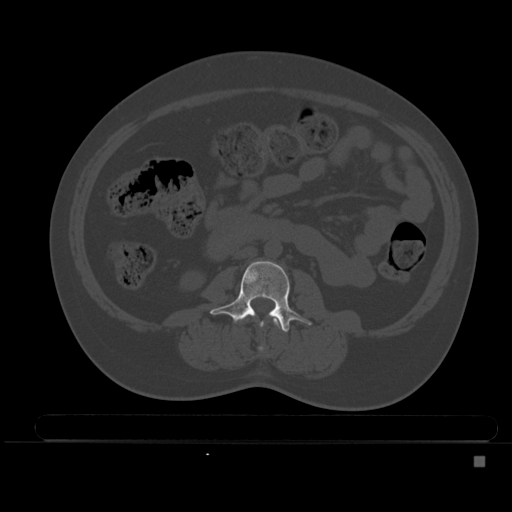
CT including the spine, one axial slice; position 155 of 495 along the scan axis; bone window (W 1800 / L 400 HU); 512 × 512 image matrix, field of view 404 × 404 mm. Female patient, age 33 years. From the clinical record (not read from this slice): primary cancer: breast; vertebrae with lytic lesions (as recorded): T1.
Annotated regions visible in this slice (semi-automatically segmented with operator editing):
- L2 vertebra: box from (x=244, y=316) to (x=283, y=351) px
- L3 vertebra: (x=210, y=261)–(x=311, y=332)